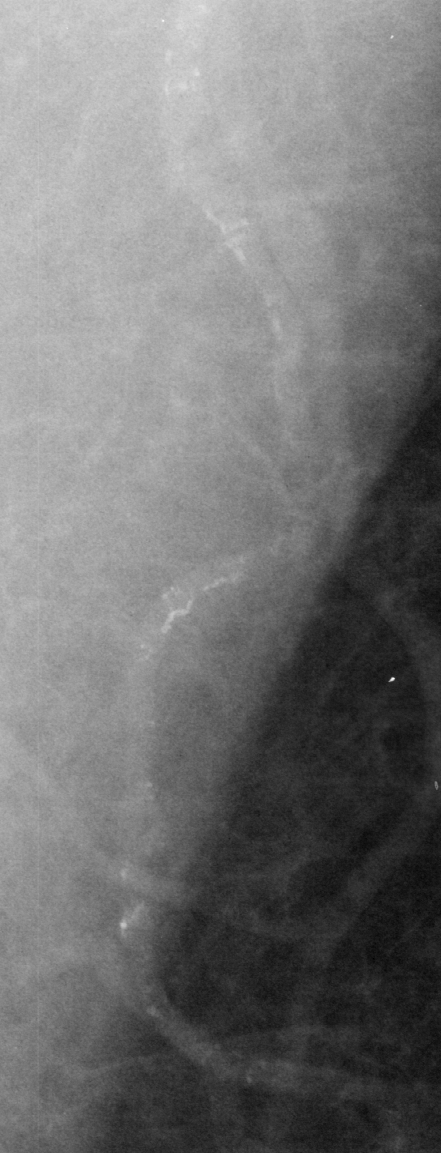
Crop from a digitized film mammogram around one marked abnormality; left breast; MLO view; BI-RADS breast density category 1 (scale 1–4).
Calcifications, morphology vascular; BI-RADS assessment category 2; subtlety rating 4 on a 1 (subtle) to 5 (obvious) scale; benign; no additional work-up was recommended (benign without callback).